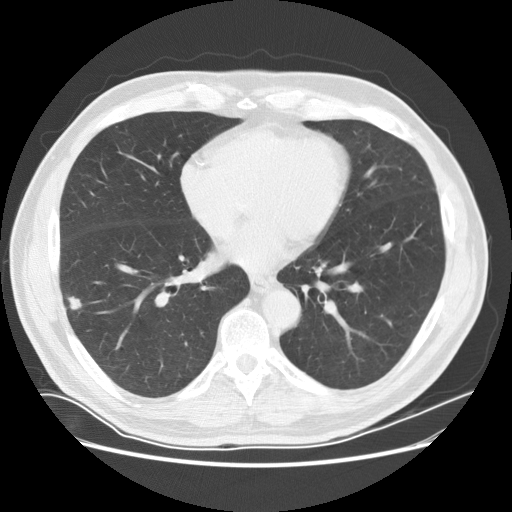
Low-dose screening chest CT, one axial slice; position 74 of 169 along the scan axis; reconstruction kernel STANDARD; 120 kVp; lung window (W 1500 / L -600 HU); 2.5 mm slice thickness; 512 × 512 image matrix.
Annotated regions visible in this slice (outlined manually by an expert reader):
- lesion 1 (tumor, lower lobe of right lung): bounding box [x1, y1, x2, y2] px = [67, 296, 82, 310]